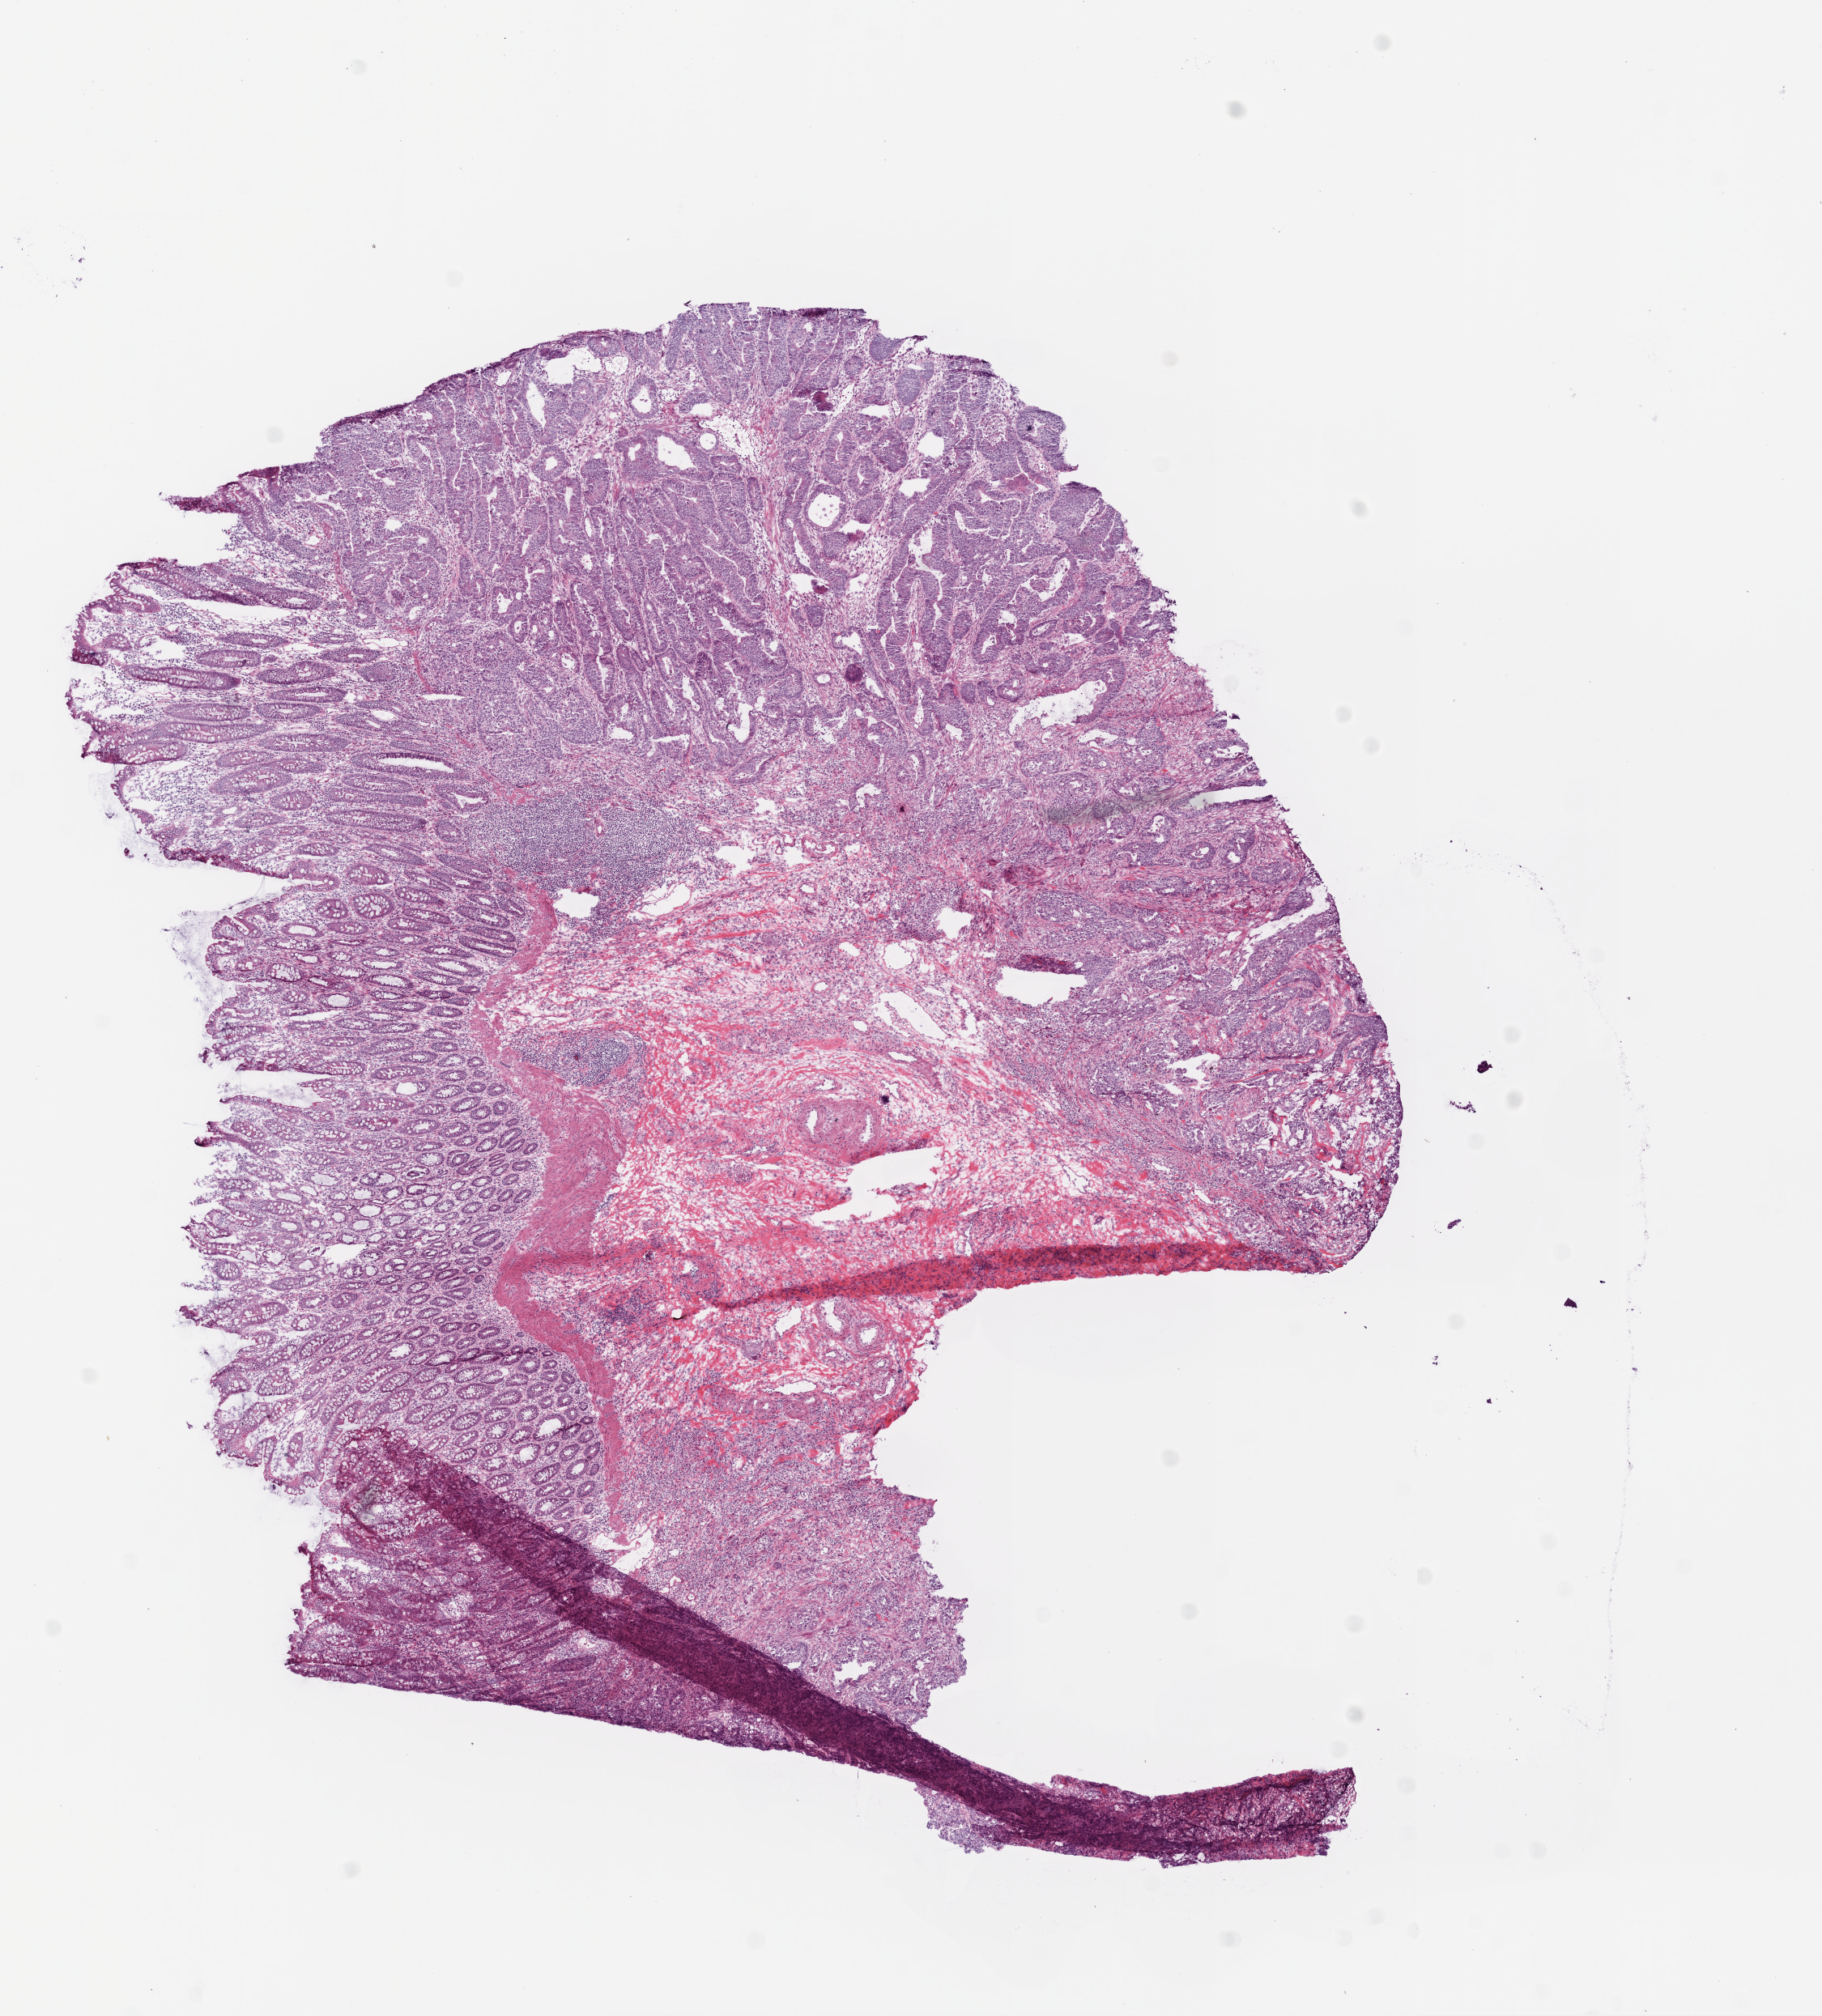
Whole-slide histology image, H&E, a low-resolution overview of the entire scanned area, about 9.0 x 10.0 mm (acquisition: 20x scan). Frozen section. Sample: primary tumour, colon. Patient: female, age at initial diagnosis 86 years. Pathologist review of this section (percent, as recorded): tumour cells 70%, tumour nuclei 90%.
Pathologic diagnosis: Adenocarcinoma, NOS (ascending colon).